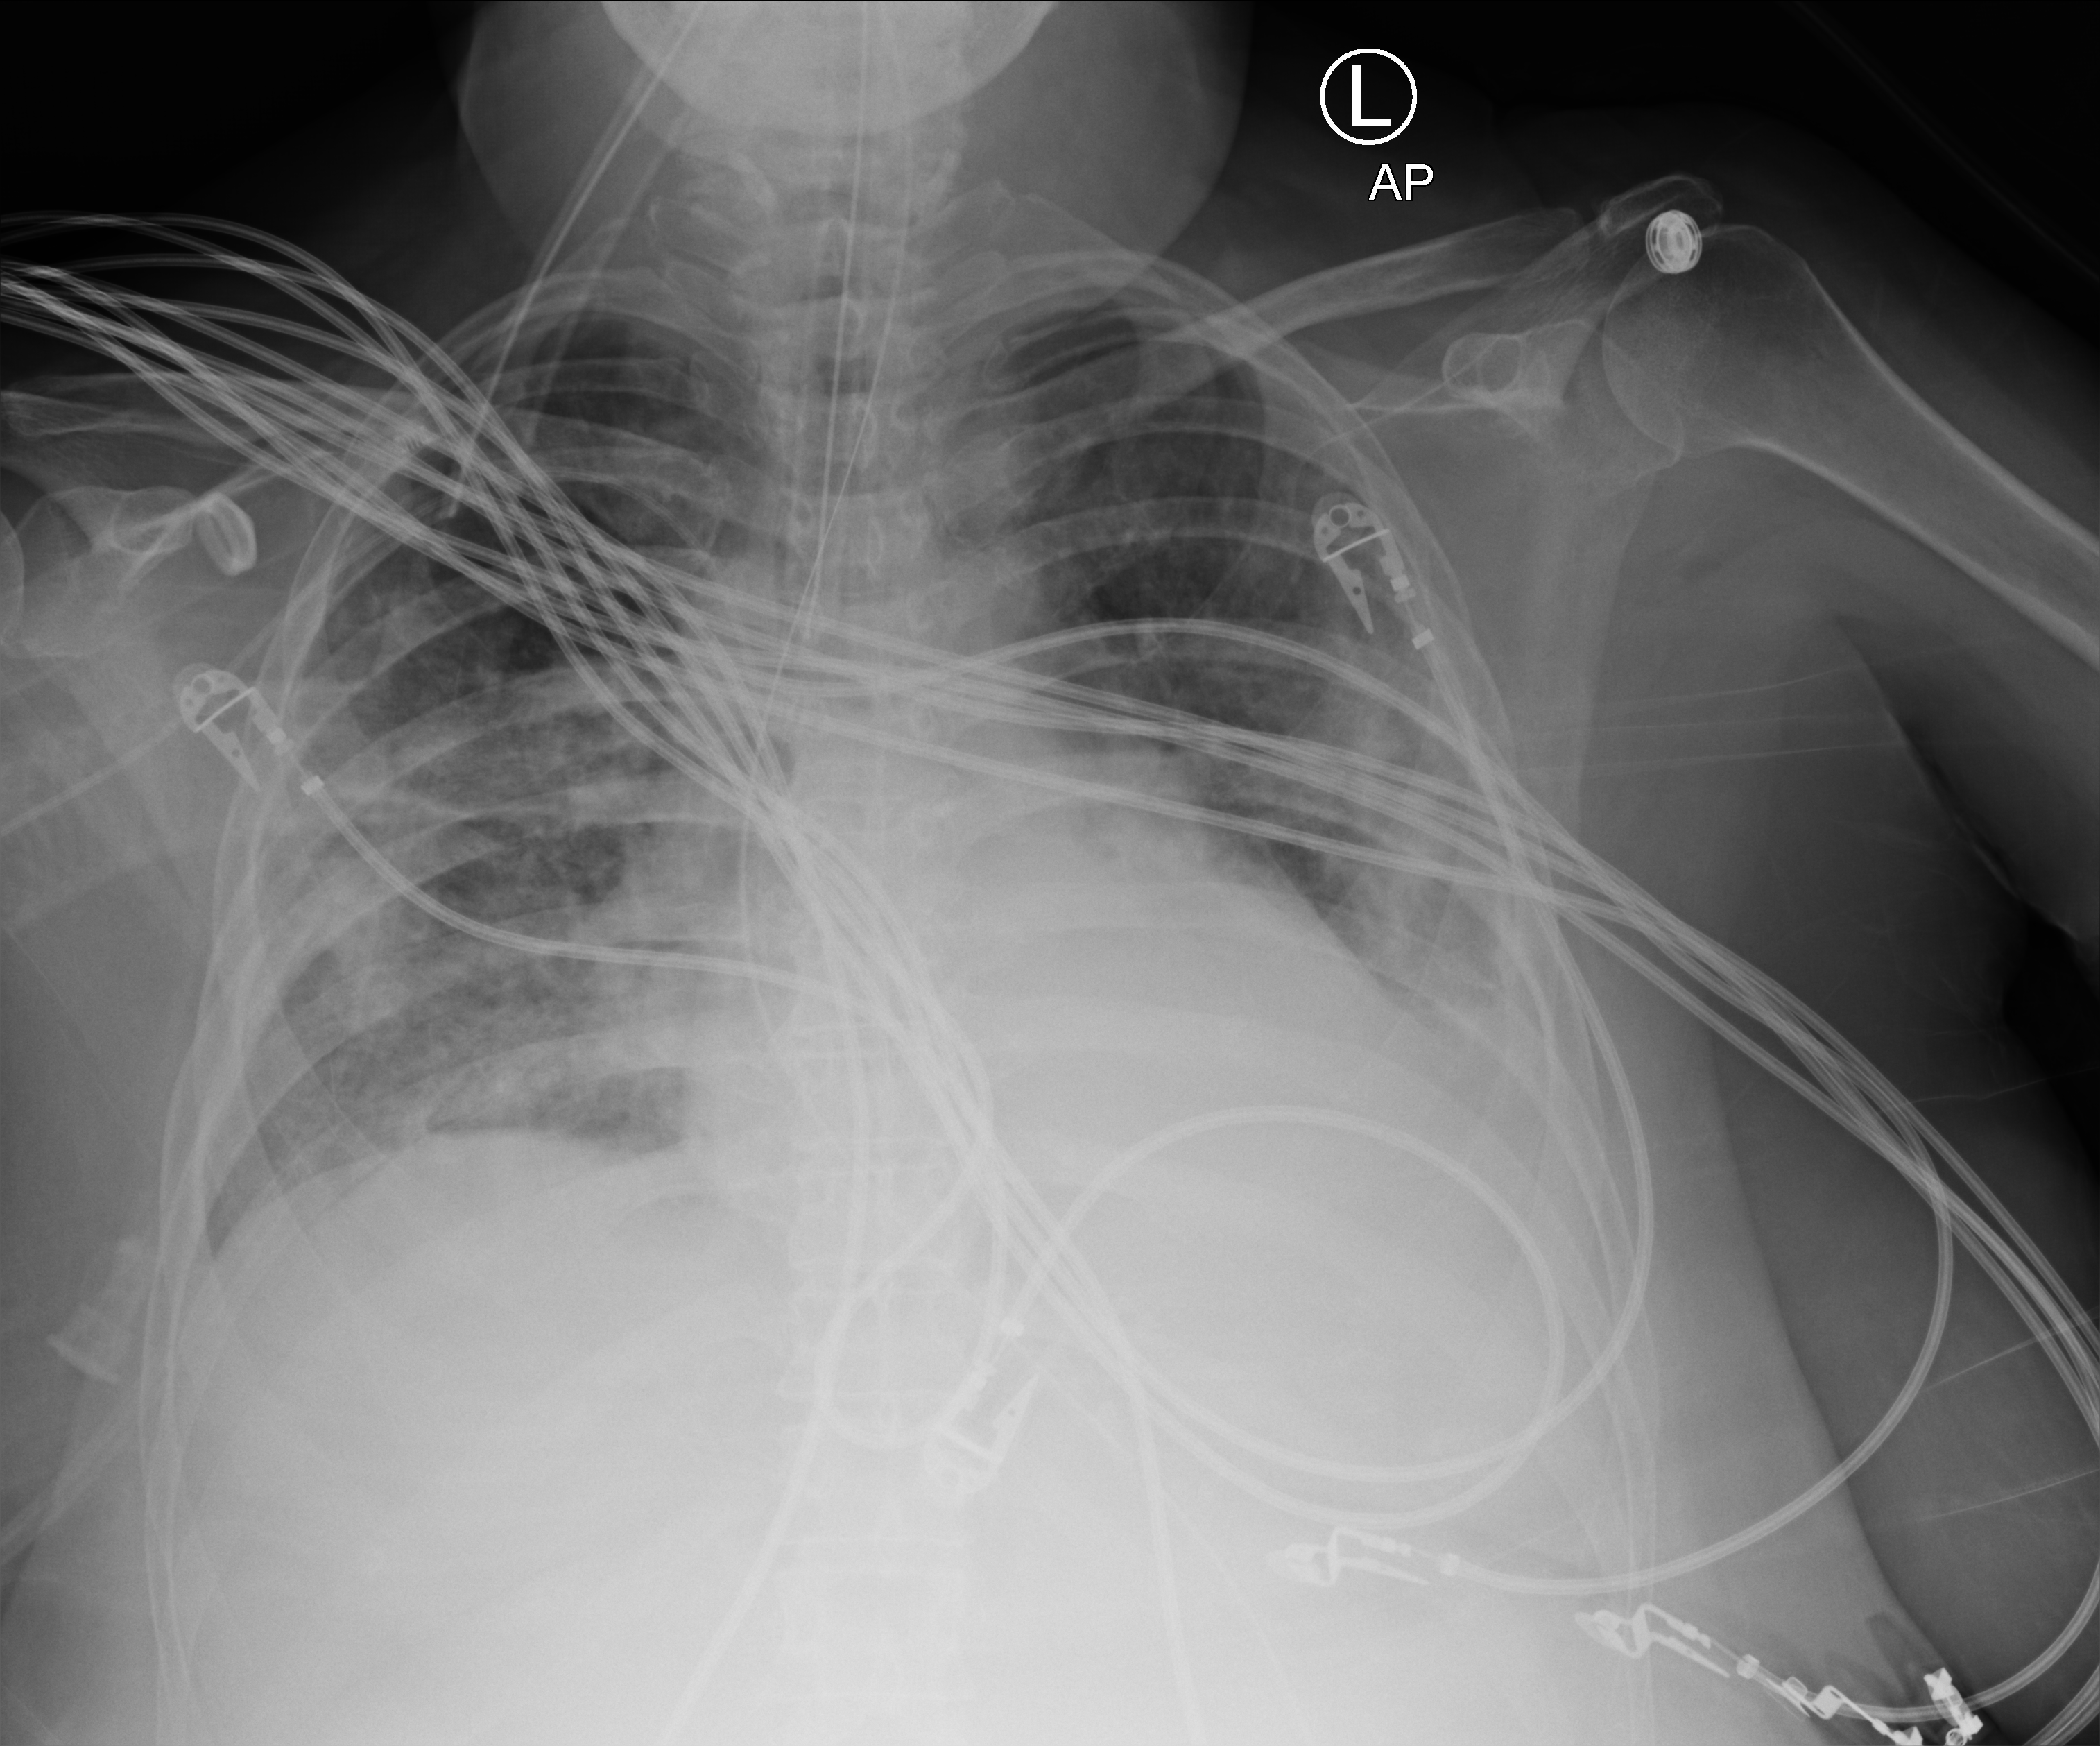
Portable chest radiograph. Female patient hospitalised with COVID-19, age 60–74 years.
From the hospital-stay record, not from the radiograph (when in the stay this image was taken is not recorded): mechanically ventilated during this hospital stay: yes; admitted to intensive care during this hospital stay: yes.